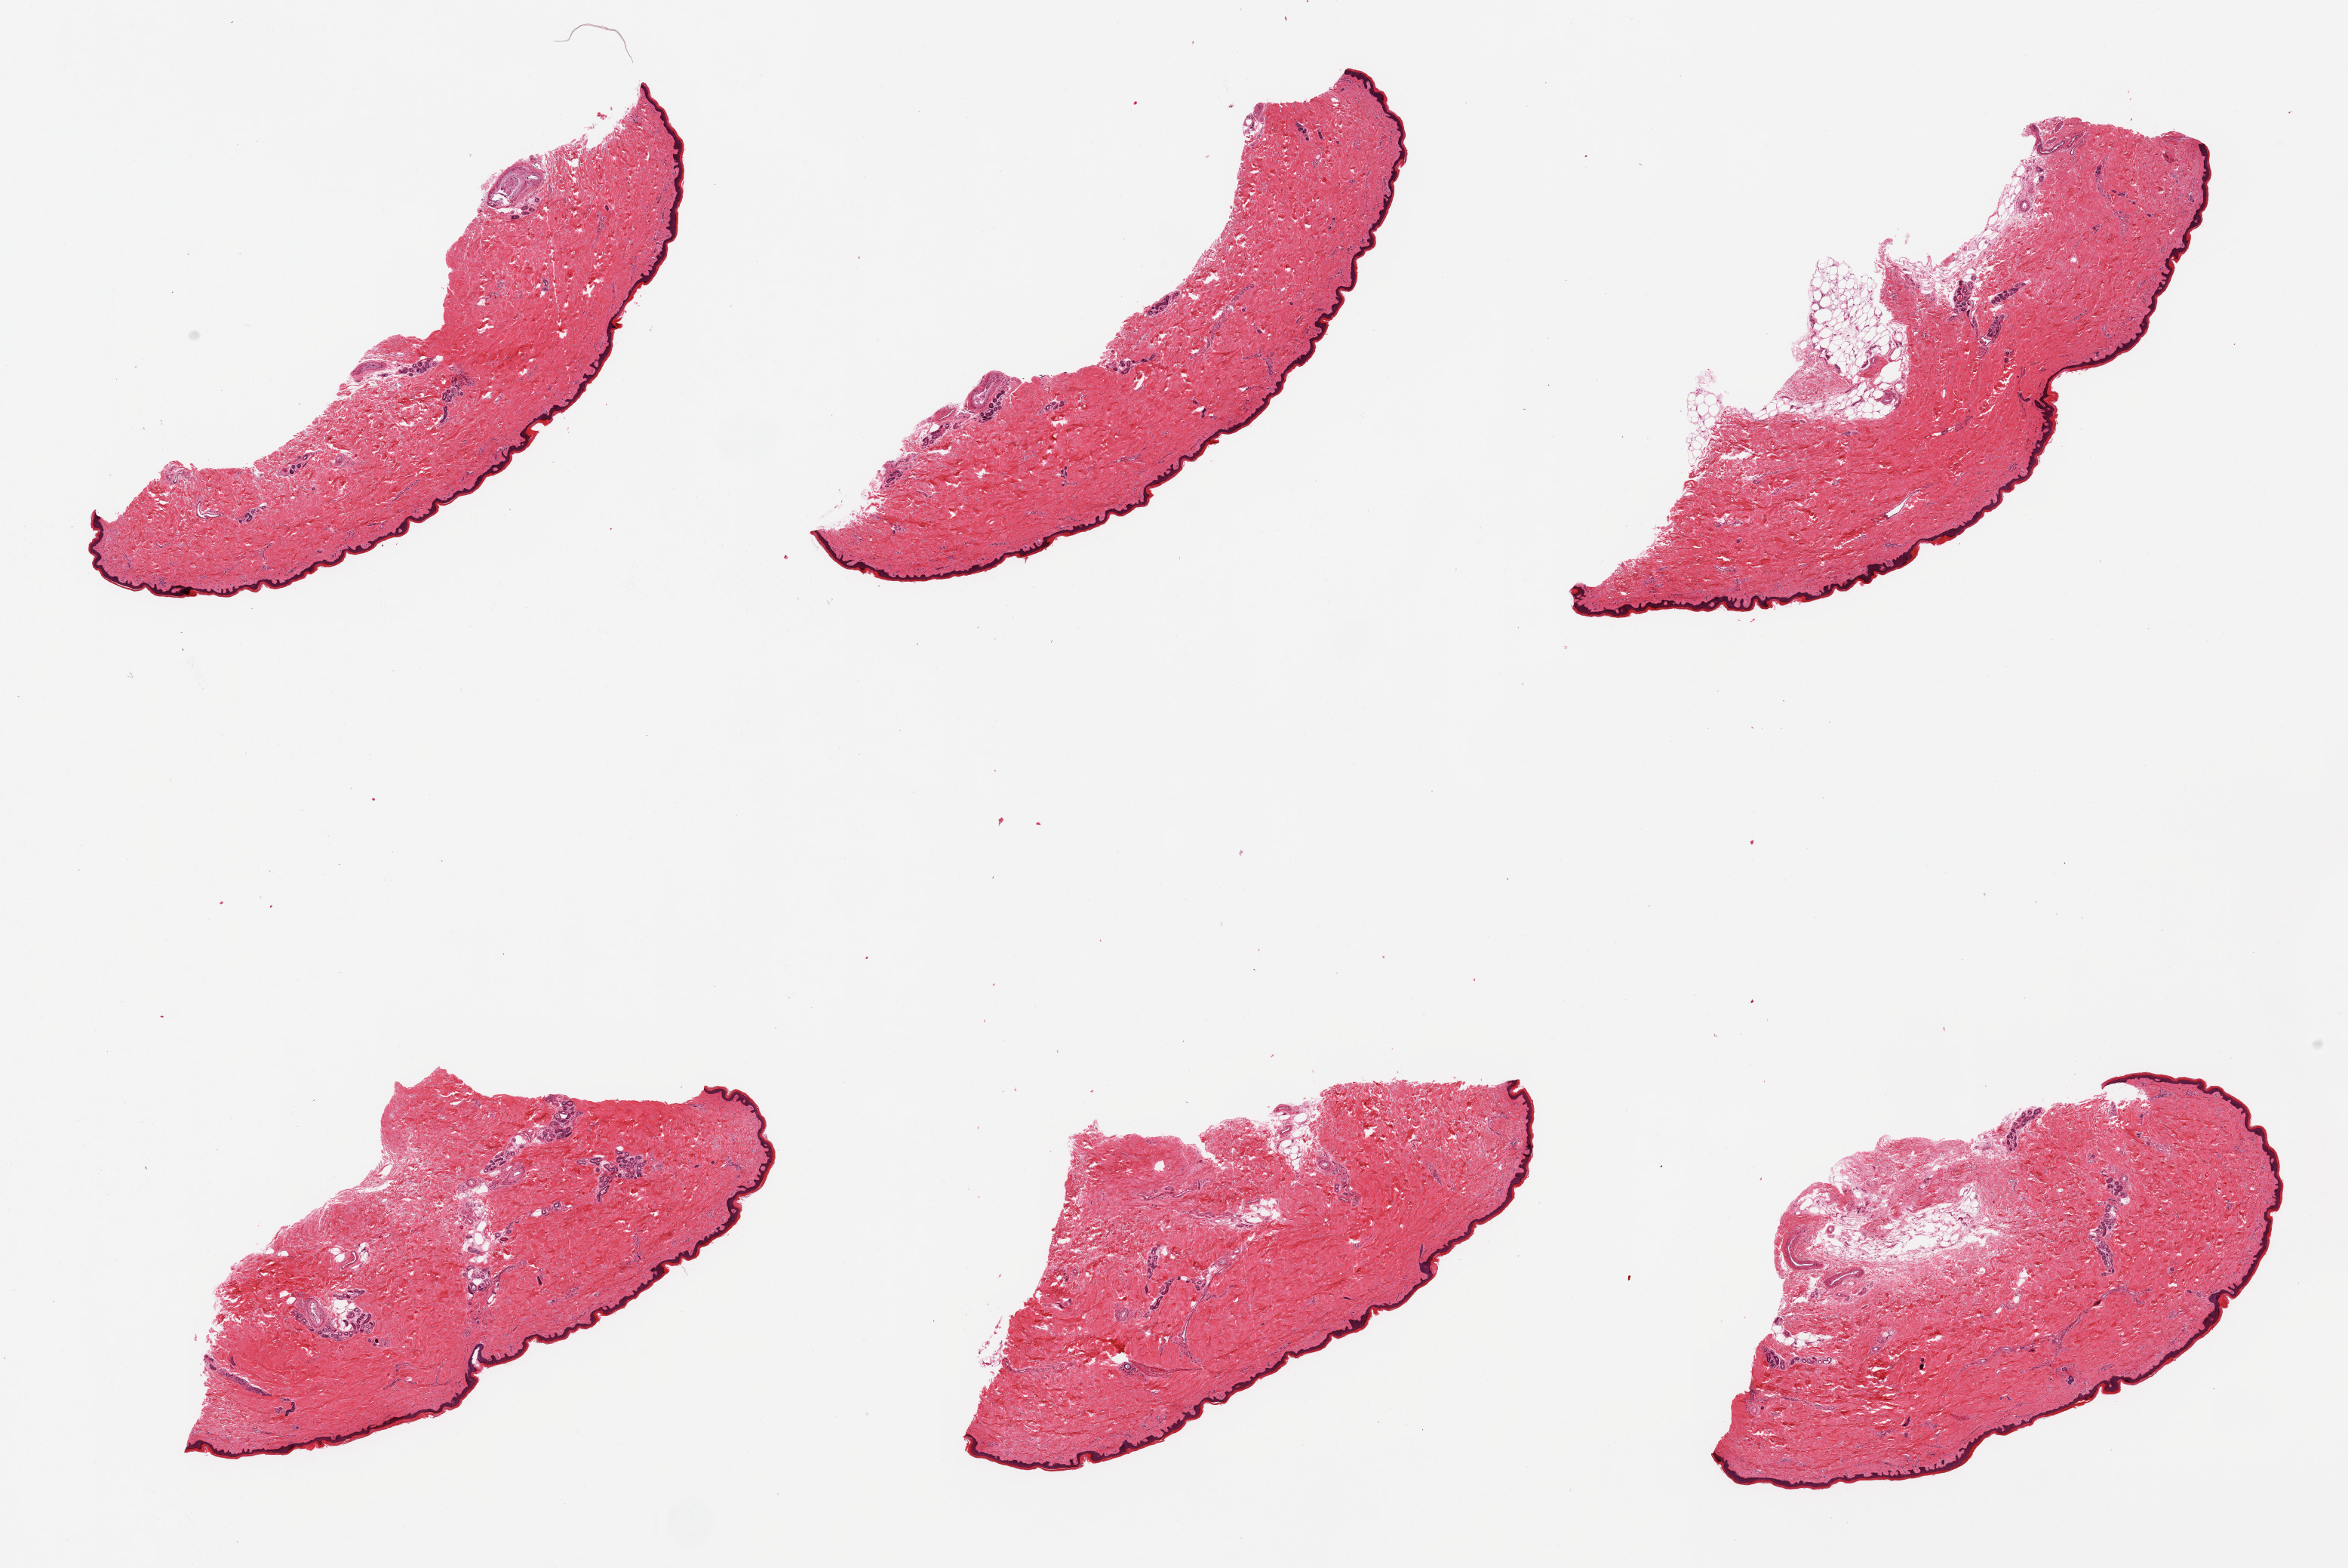
Digitized haematoxylin and eosin-stained section — shown as a low-resolution overview of the whole scanned area (about 24.6 x 16.4 mm), PAXgene-fixed paraffin-embedded (PFPE) section, target tissue: skin of lower leg, tissue donor sample. Female donor.
• reviewer comment on this tissue sample: 6 pieces, minimal dermal fat. Squamous epithelium is ~45-50 microns